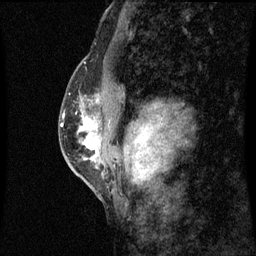
Breast MRI (dynamic contrast-enhanced), one sagittal slice. Slice 36 of 60 in the series (ordered by position). Dynamic contrast-enhanced series, image 2 of 3 at this slice position (ordered by acquisition). 1.5 T. TE 4.2 ms, TR 8.9 ms. 2 mm slice thickness. 256 × 256 image matrix. Female patient, age 50 years. From the clinical record (not read from this slice): setting: breast cancer imaged before/during neoadjuvant chemotherapy; receptor status: triple-negative.
Structures marked on this image (semi-automatic segmentation, software-assisted and operator-edited):
- analysis volume of interest (the breast-tissue region the enhancement analysis was run in; not a lesion): box from (x=68, y=80) to (x=101, y=169) px
- tumour enhancement mask (voxels above the 70 % enhancement threshold inside the analysis volume of interest): (x=81, y=118)–(x=98, y=161)